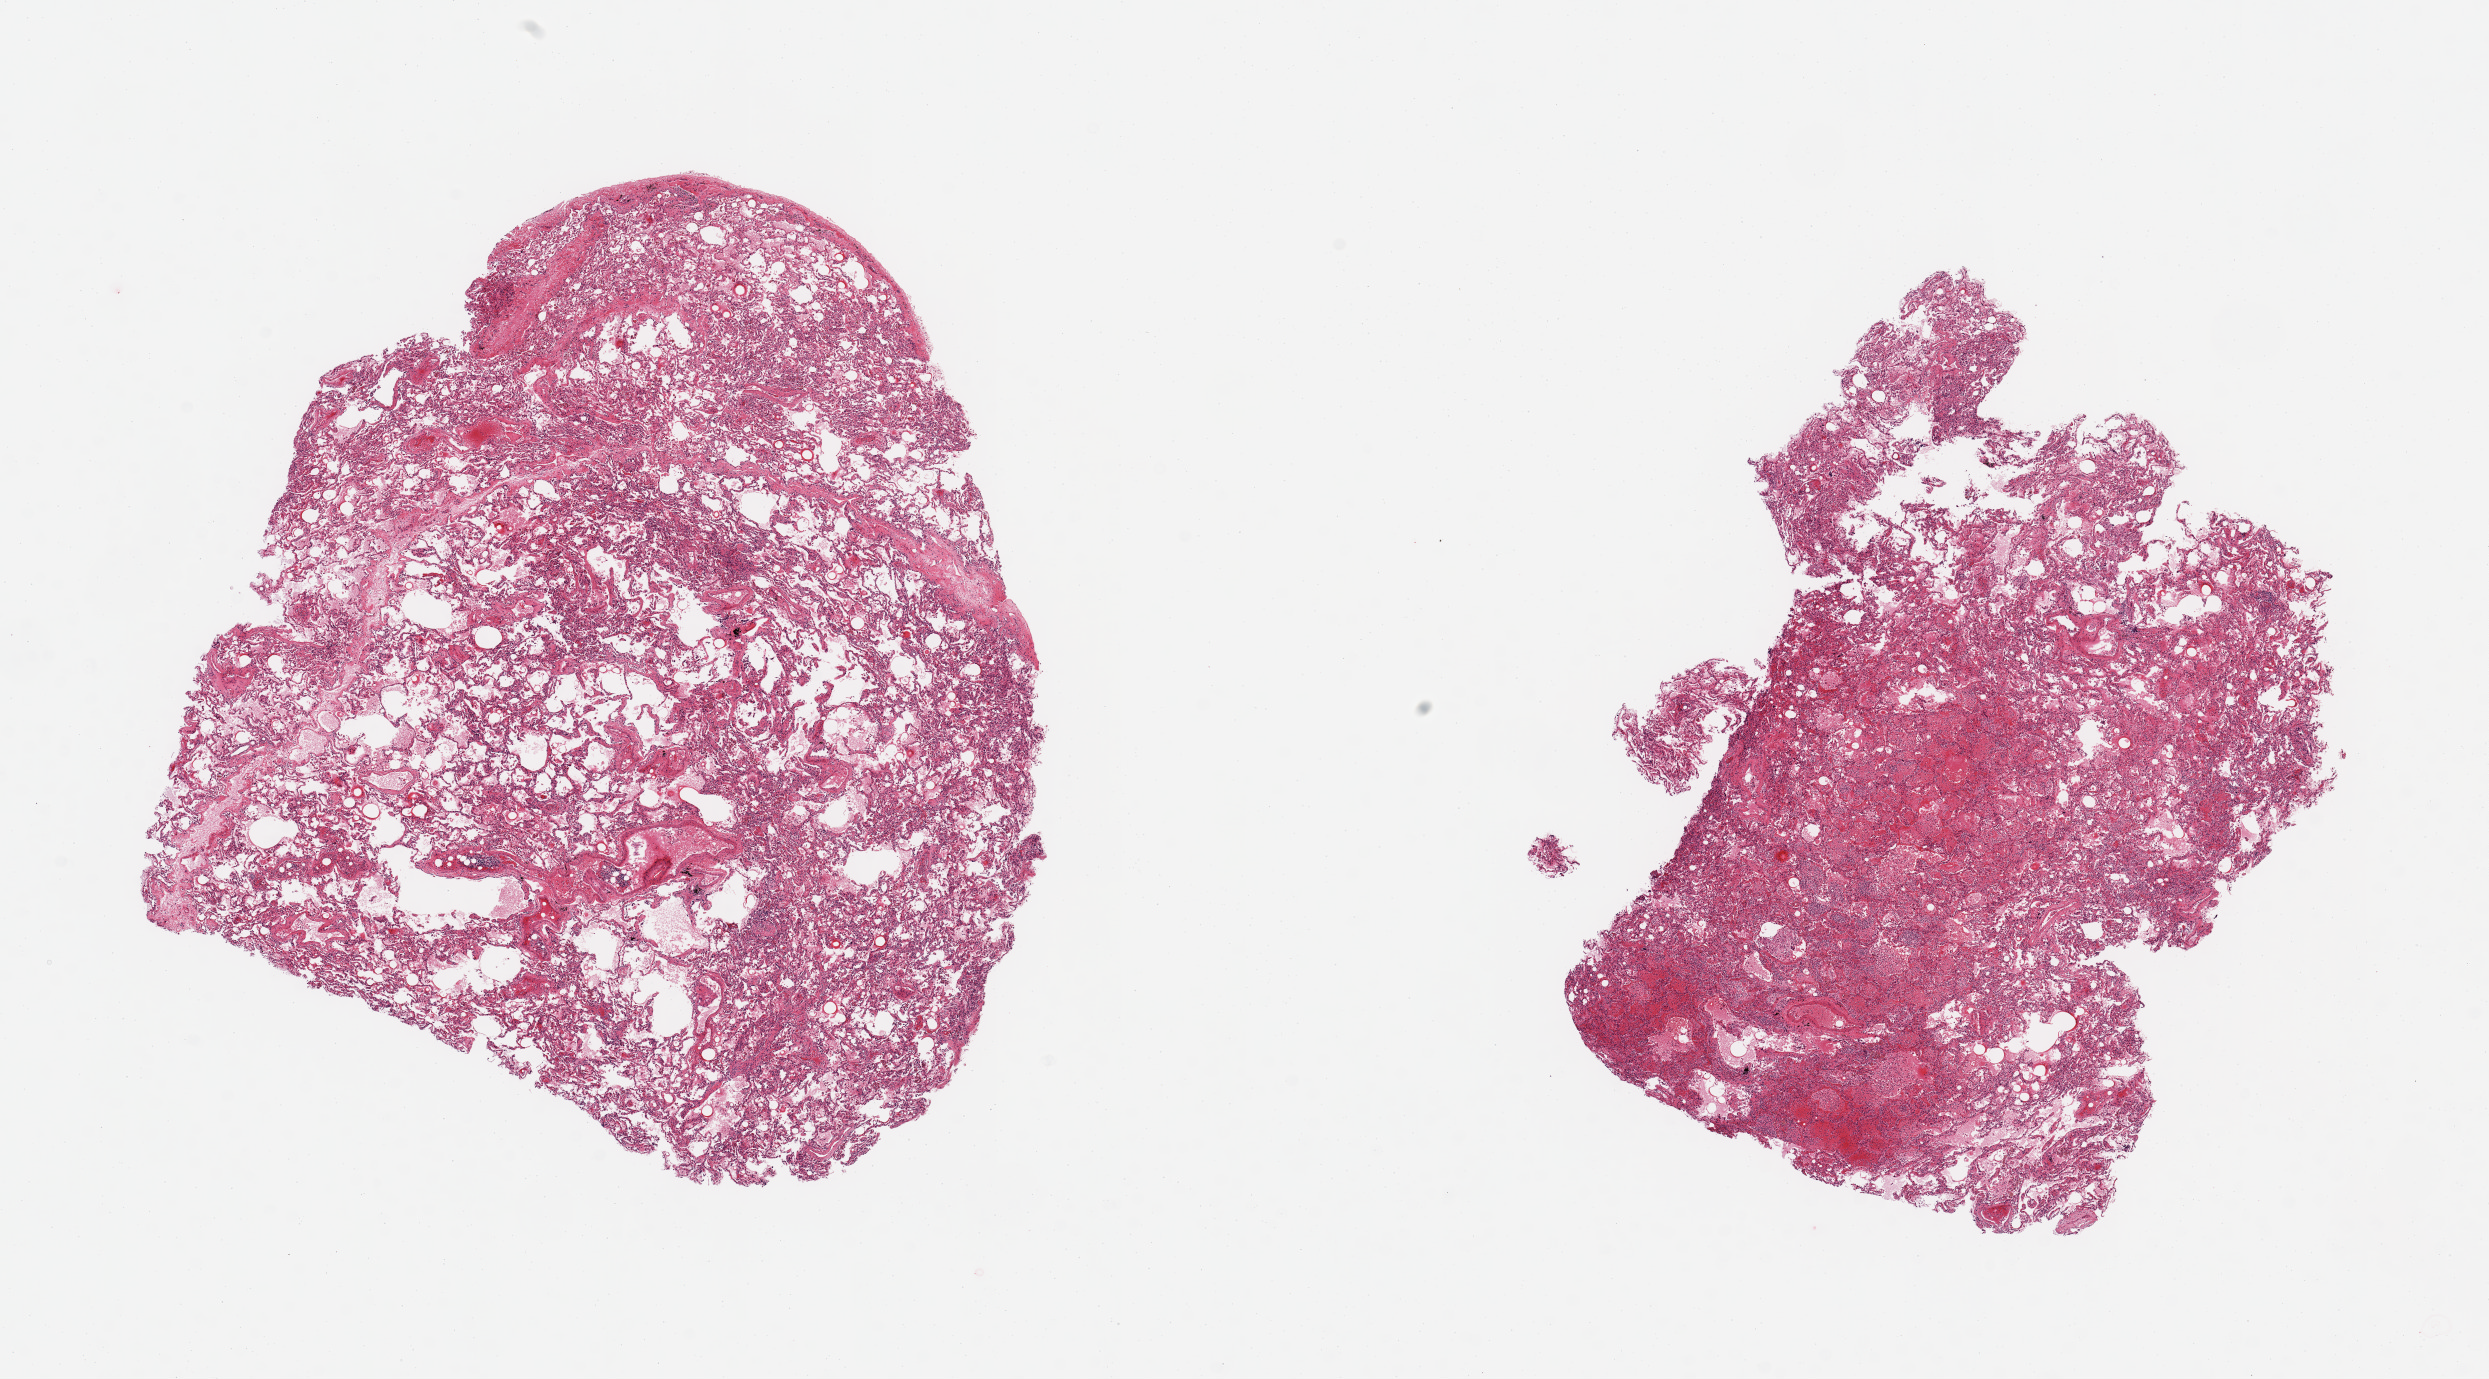
Whole-slide image, hematoxylin and eosin (H&E) stain, low-resolution overview of the scanned area, about 19.7 x 10.9 mm (from a 20x scan). PAXgene-fixed paraffin-embedded (PFPE) section. Section of lung (target tissue). Tissue donor sample. Donor sex: male.
• pathologist's review note for this sample: 2 pieces, patchy acute/chronic pneumonitis, hemmorhagic, moderate congestion